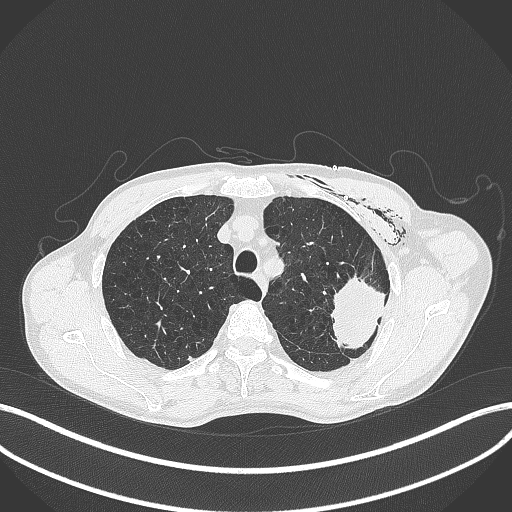
Chest CT, one axial slice. Position 324 of 457 along the scan axis. Reconstruction kernel B70f. Lung window (W 1500 / L -600 HU). 1 mm slice thickness. 512 × 512 image matrix, field of view 400 × 400 mm. Patient: male, 58 years. Case-level facts recorded for this patient, not image findings: clinical TNM (as recorded): T3 N0 M0.
Outlined on this slice (bounding box drawn by a radiologist):
- lung tumour (recorded histology: adenocarcinoma): box from (x=326, y=269) to (x=388, y=357) px